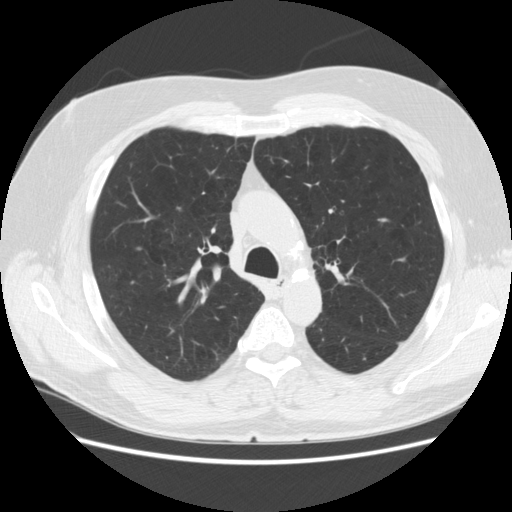
Chest CT (low-dose screening protocol), one axial image, baseline annual screen, lung window (W 1500 / L -600 HU), 2.5 mm slice thickness, standard (soft-tissue) reconstruction kernel (STANDARD), 120 kVp. Male participant, aged 63 years at enrolment. Former smoker at enrolment.
Expert reader's lesion annotation, bounding box (x1, y1, x2, y2) in pixels: (166, 200, 197, 225). No non-calcified nodule or mass ≥4 mm was recorded by the screening reader at this exam. Later outcome: lung cancer diagnosed 1085 days after this screen — adenocarcinoma, NOS, right upper lobe, stage IIA (AJCC 6th edition), 8 mm at pathology.